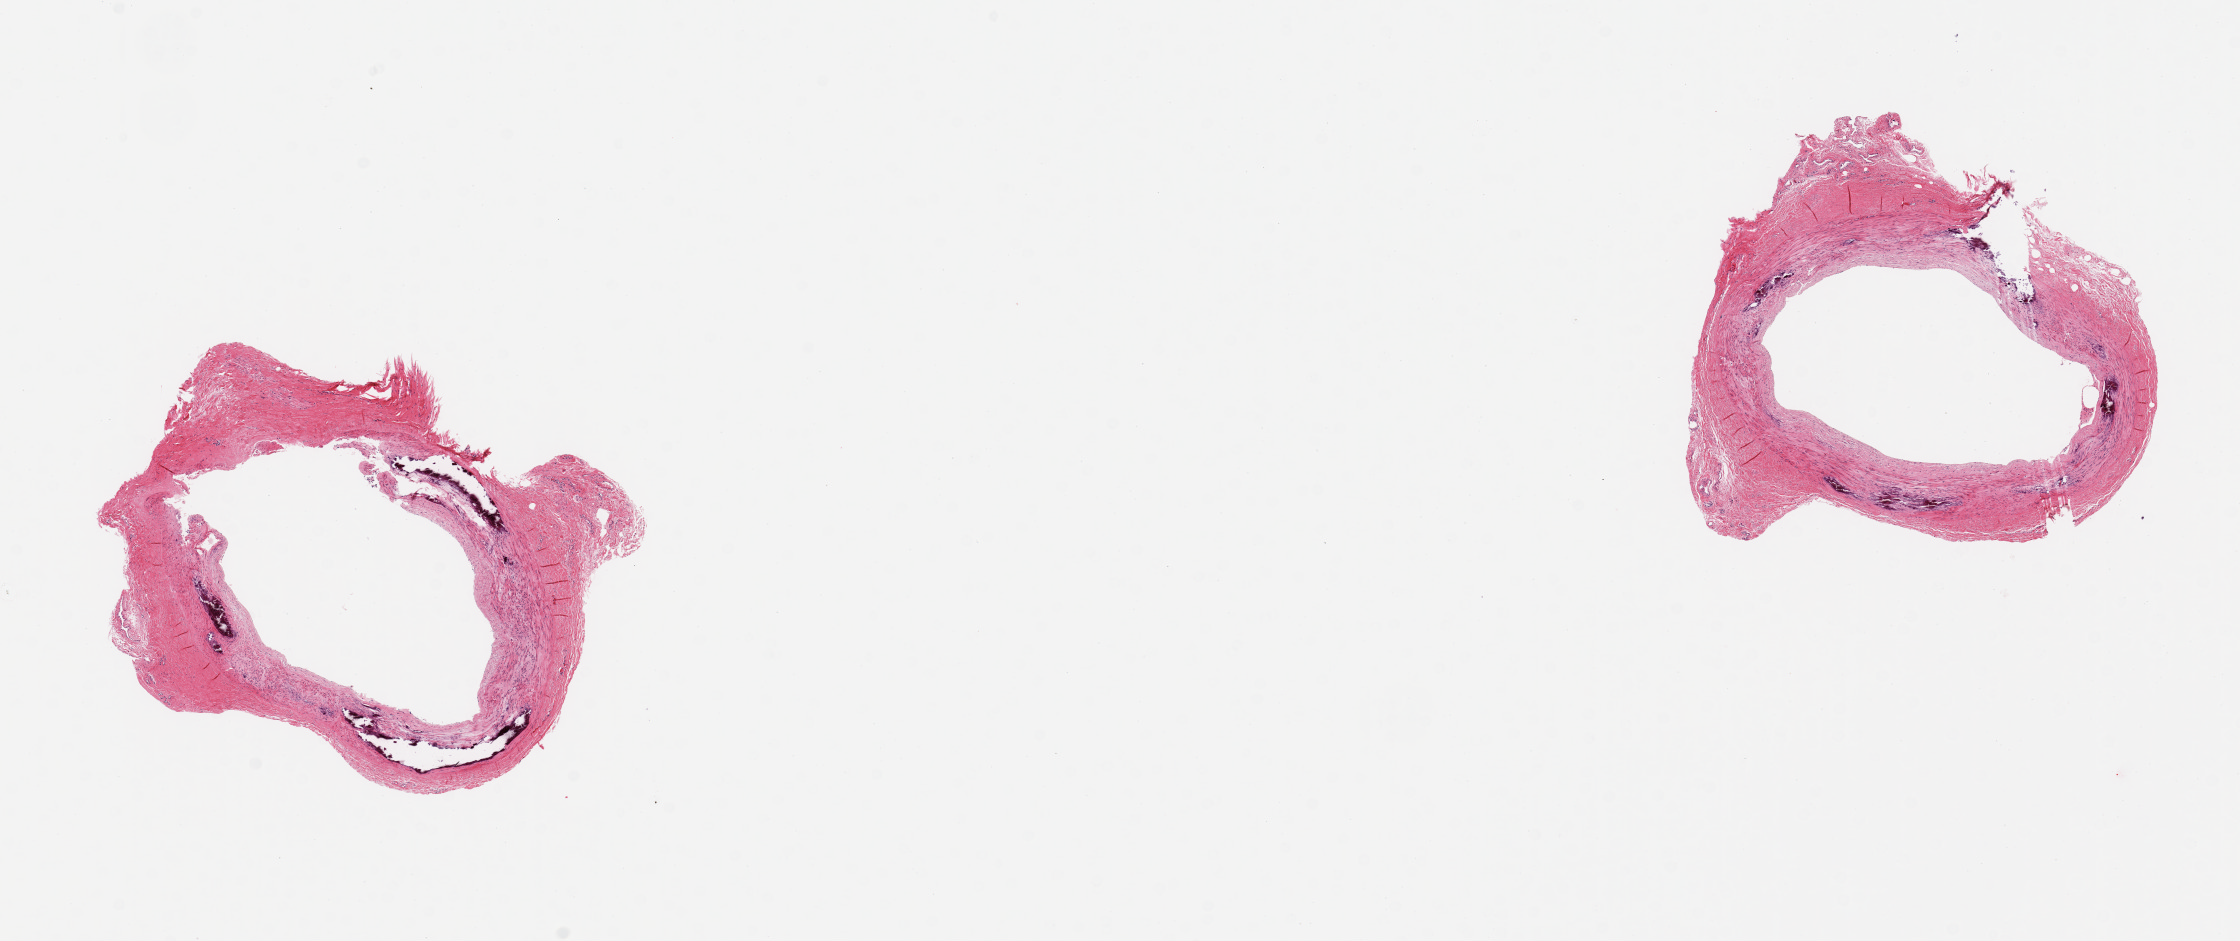
H&E whole-slide image, whole scanned area (about 17.7 x 7.4 mm) shown as a low-resolution overview. PAXgene-fixed paraffin-embedded (PFPE) section. Target tissue: tibial artery. Donor tissue sample. Male donor.
Reviewer comment on this tissue sample: 2 pieces, minimal atherosis, adherent fat; Monckeberg medial sclerosis present, rep focidelineated.